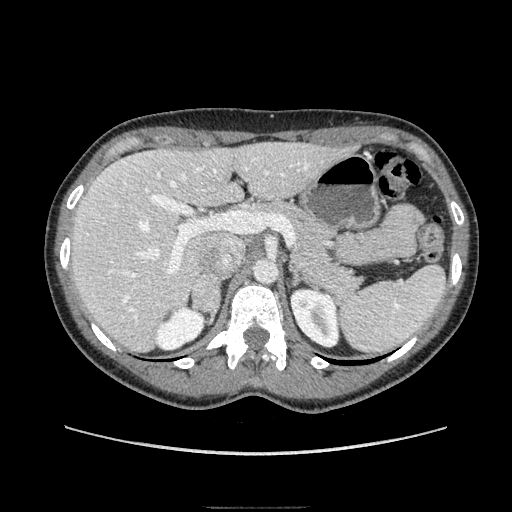
Contrast-enhanced abdominal CT, one axial slice. Position 115 of 193 along the scan axis. Soft-tissue window (W 400 / L 40 HU). 1.25 mm slice thickness. 512 × 512 image matrix, field of view 380 × 380 mm. Female patient. From the clinical record (not read from this slice): diagnosis: adrenocortical carcinoma; tumour side: right adrenal; tumour size at pathology: 3 cm; Ki-67 index: 4 %; stage (as recorded): 1.
Annotated regions visible in this slice (semi-automatically segmented with operator editing):
- mass: bounding box (x1, y1, x2, y2) in pixels: (194, 275, 219, 319)